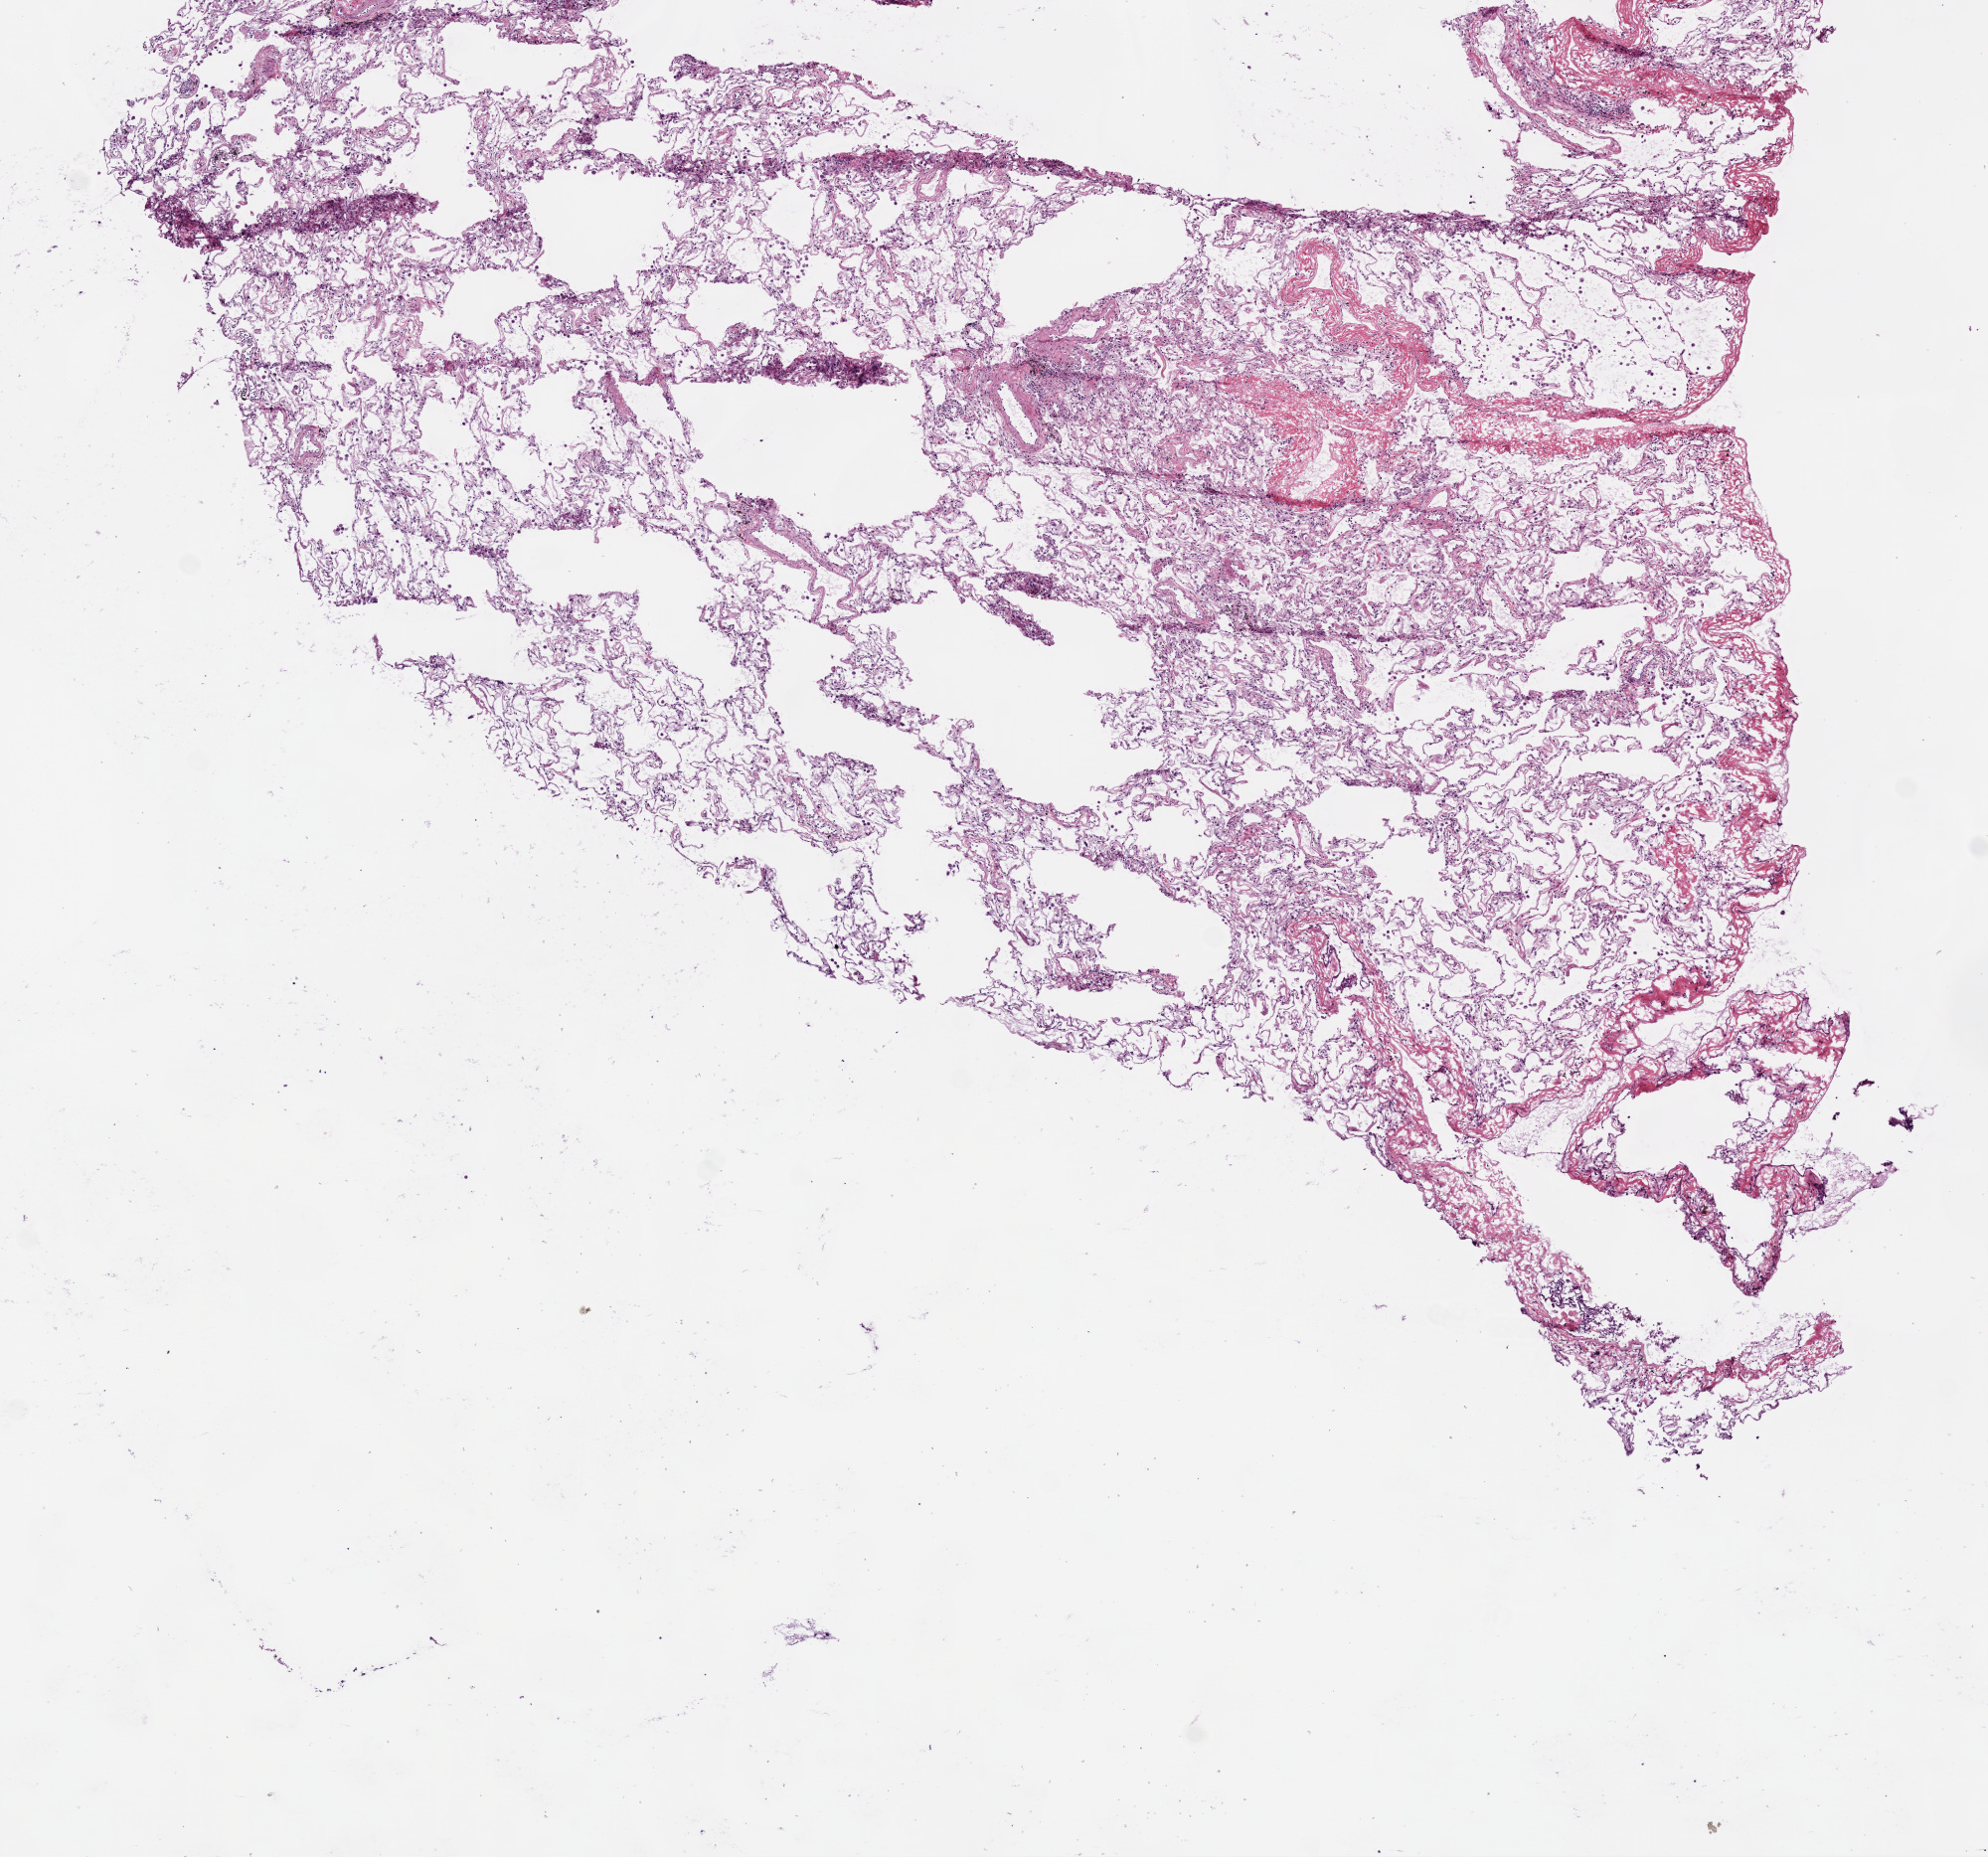
Digitized Hematoxylin and eosin (H&E) stained tissue section (whole slide) — shown as a low-resolution overview of the whole scanned area (about 8.0 x 7.5 mm). Frozen section. Sample: solid tissue normal (non-tumour tissue), lung. Female, age 65 years at initial diagnosis.
* this section: solid tissue normal (non-tumour) sample from the same patient
* patient diagnosis: Adenocarcinoma, NOS (upper lobe, lung)